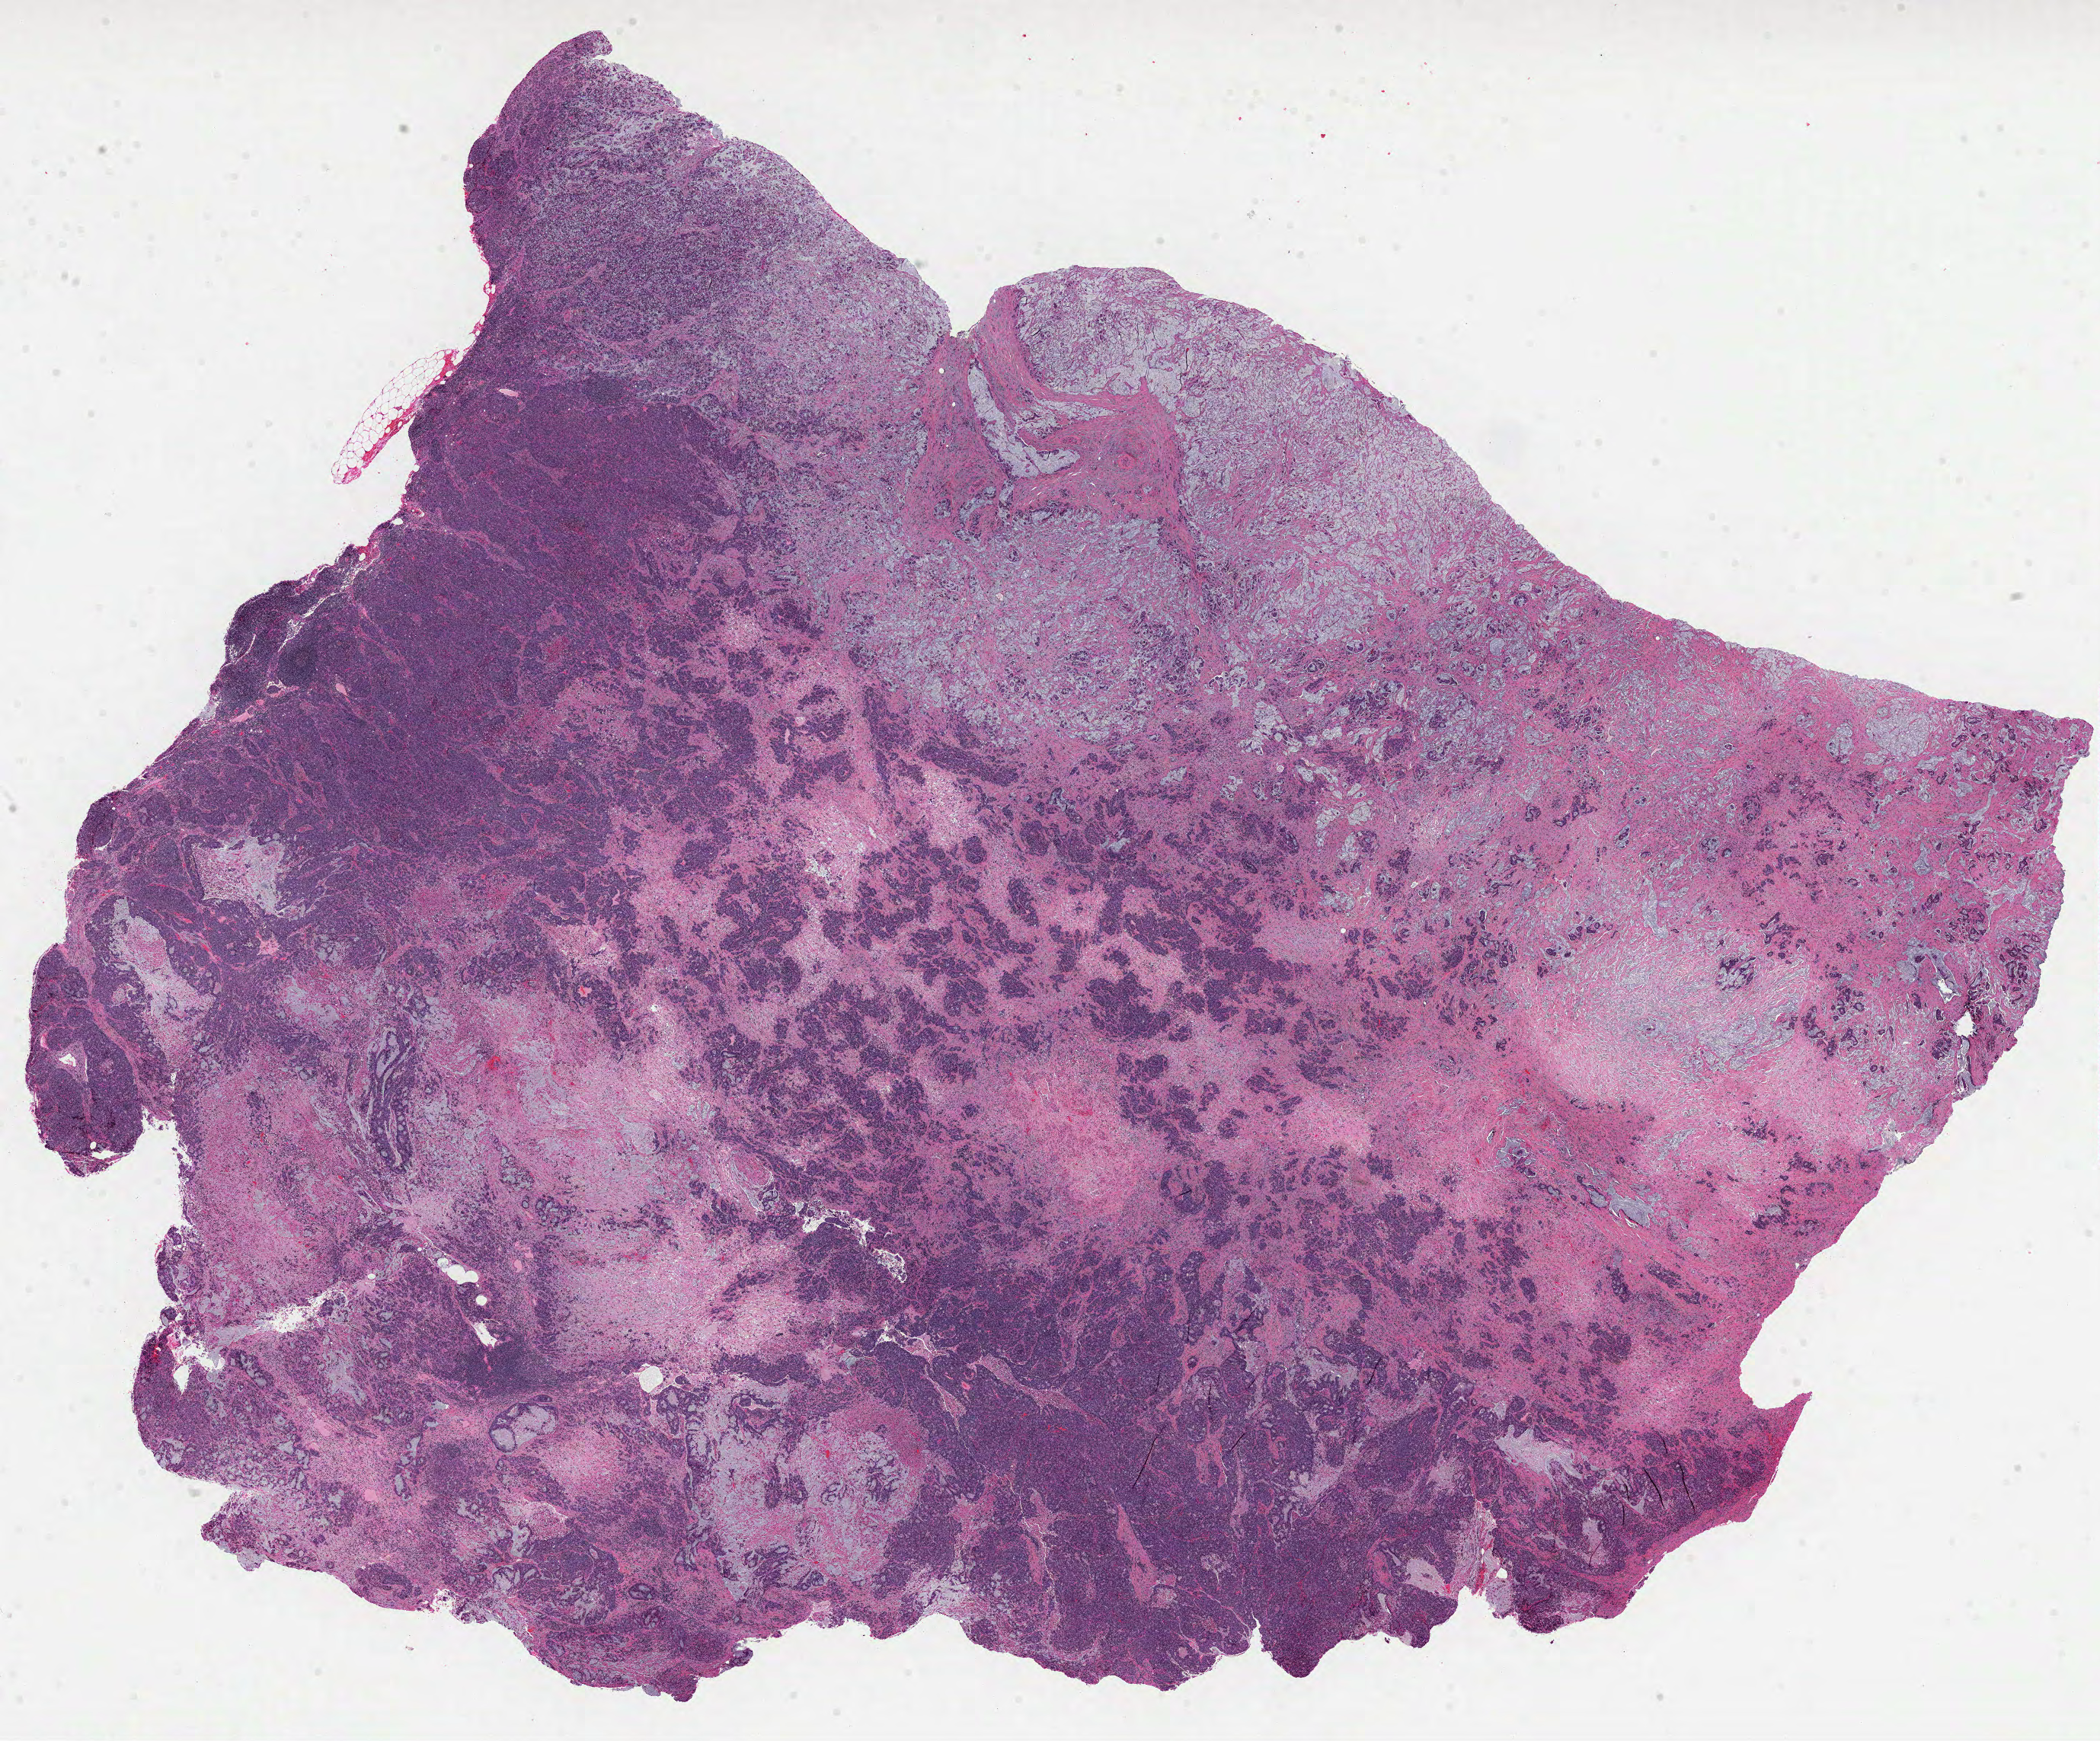
Whole-slide histology image, Hematoxylin and eosin (H&E) stained — shown as a low-resolution overview of the whole scanned area (about 22.2 x 18.4 mm), formalin-fixed paraffin-embedded (FFPE) diagnostic section, colon, primary tumour sample. Male, age 47 years at initial diagnosis.
AJCC pathologic stage: IIIC (7th edition). Lymph nodes positive (case pathology): 12 of 14 examined. Diagnosis: Mucinous adenocarcinoma (ascending colon).